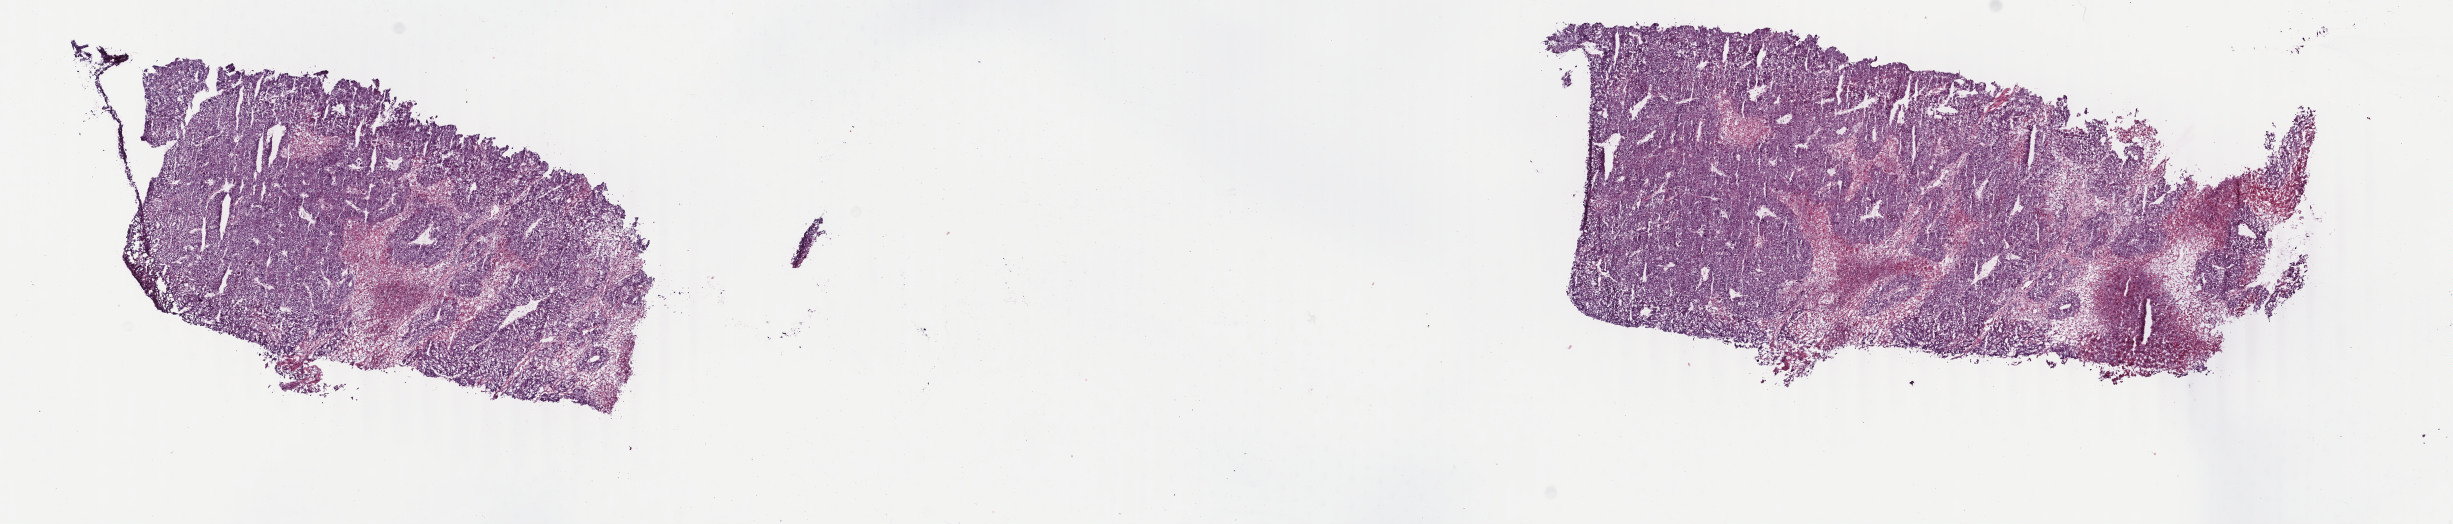
Hematoxylin and eosin (H&E) stained whole-slide image — whole scanned area (about 19.5 x 4.2 mm) shown as a low-resolution overview, frozen section from the top of the tissue portion, liver, primary tumour sample. Male patient; age at initial diagnosis 60 years.
Pathologic diagnosis: Hepatocellular carcinoma, NOS.